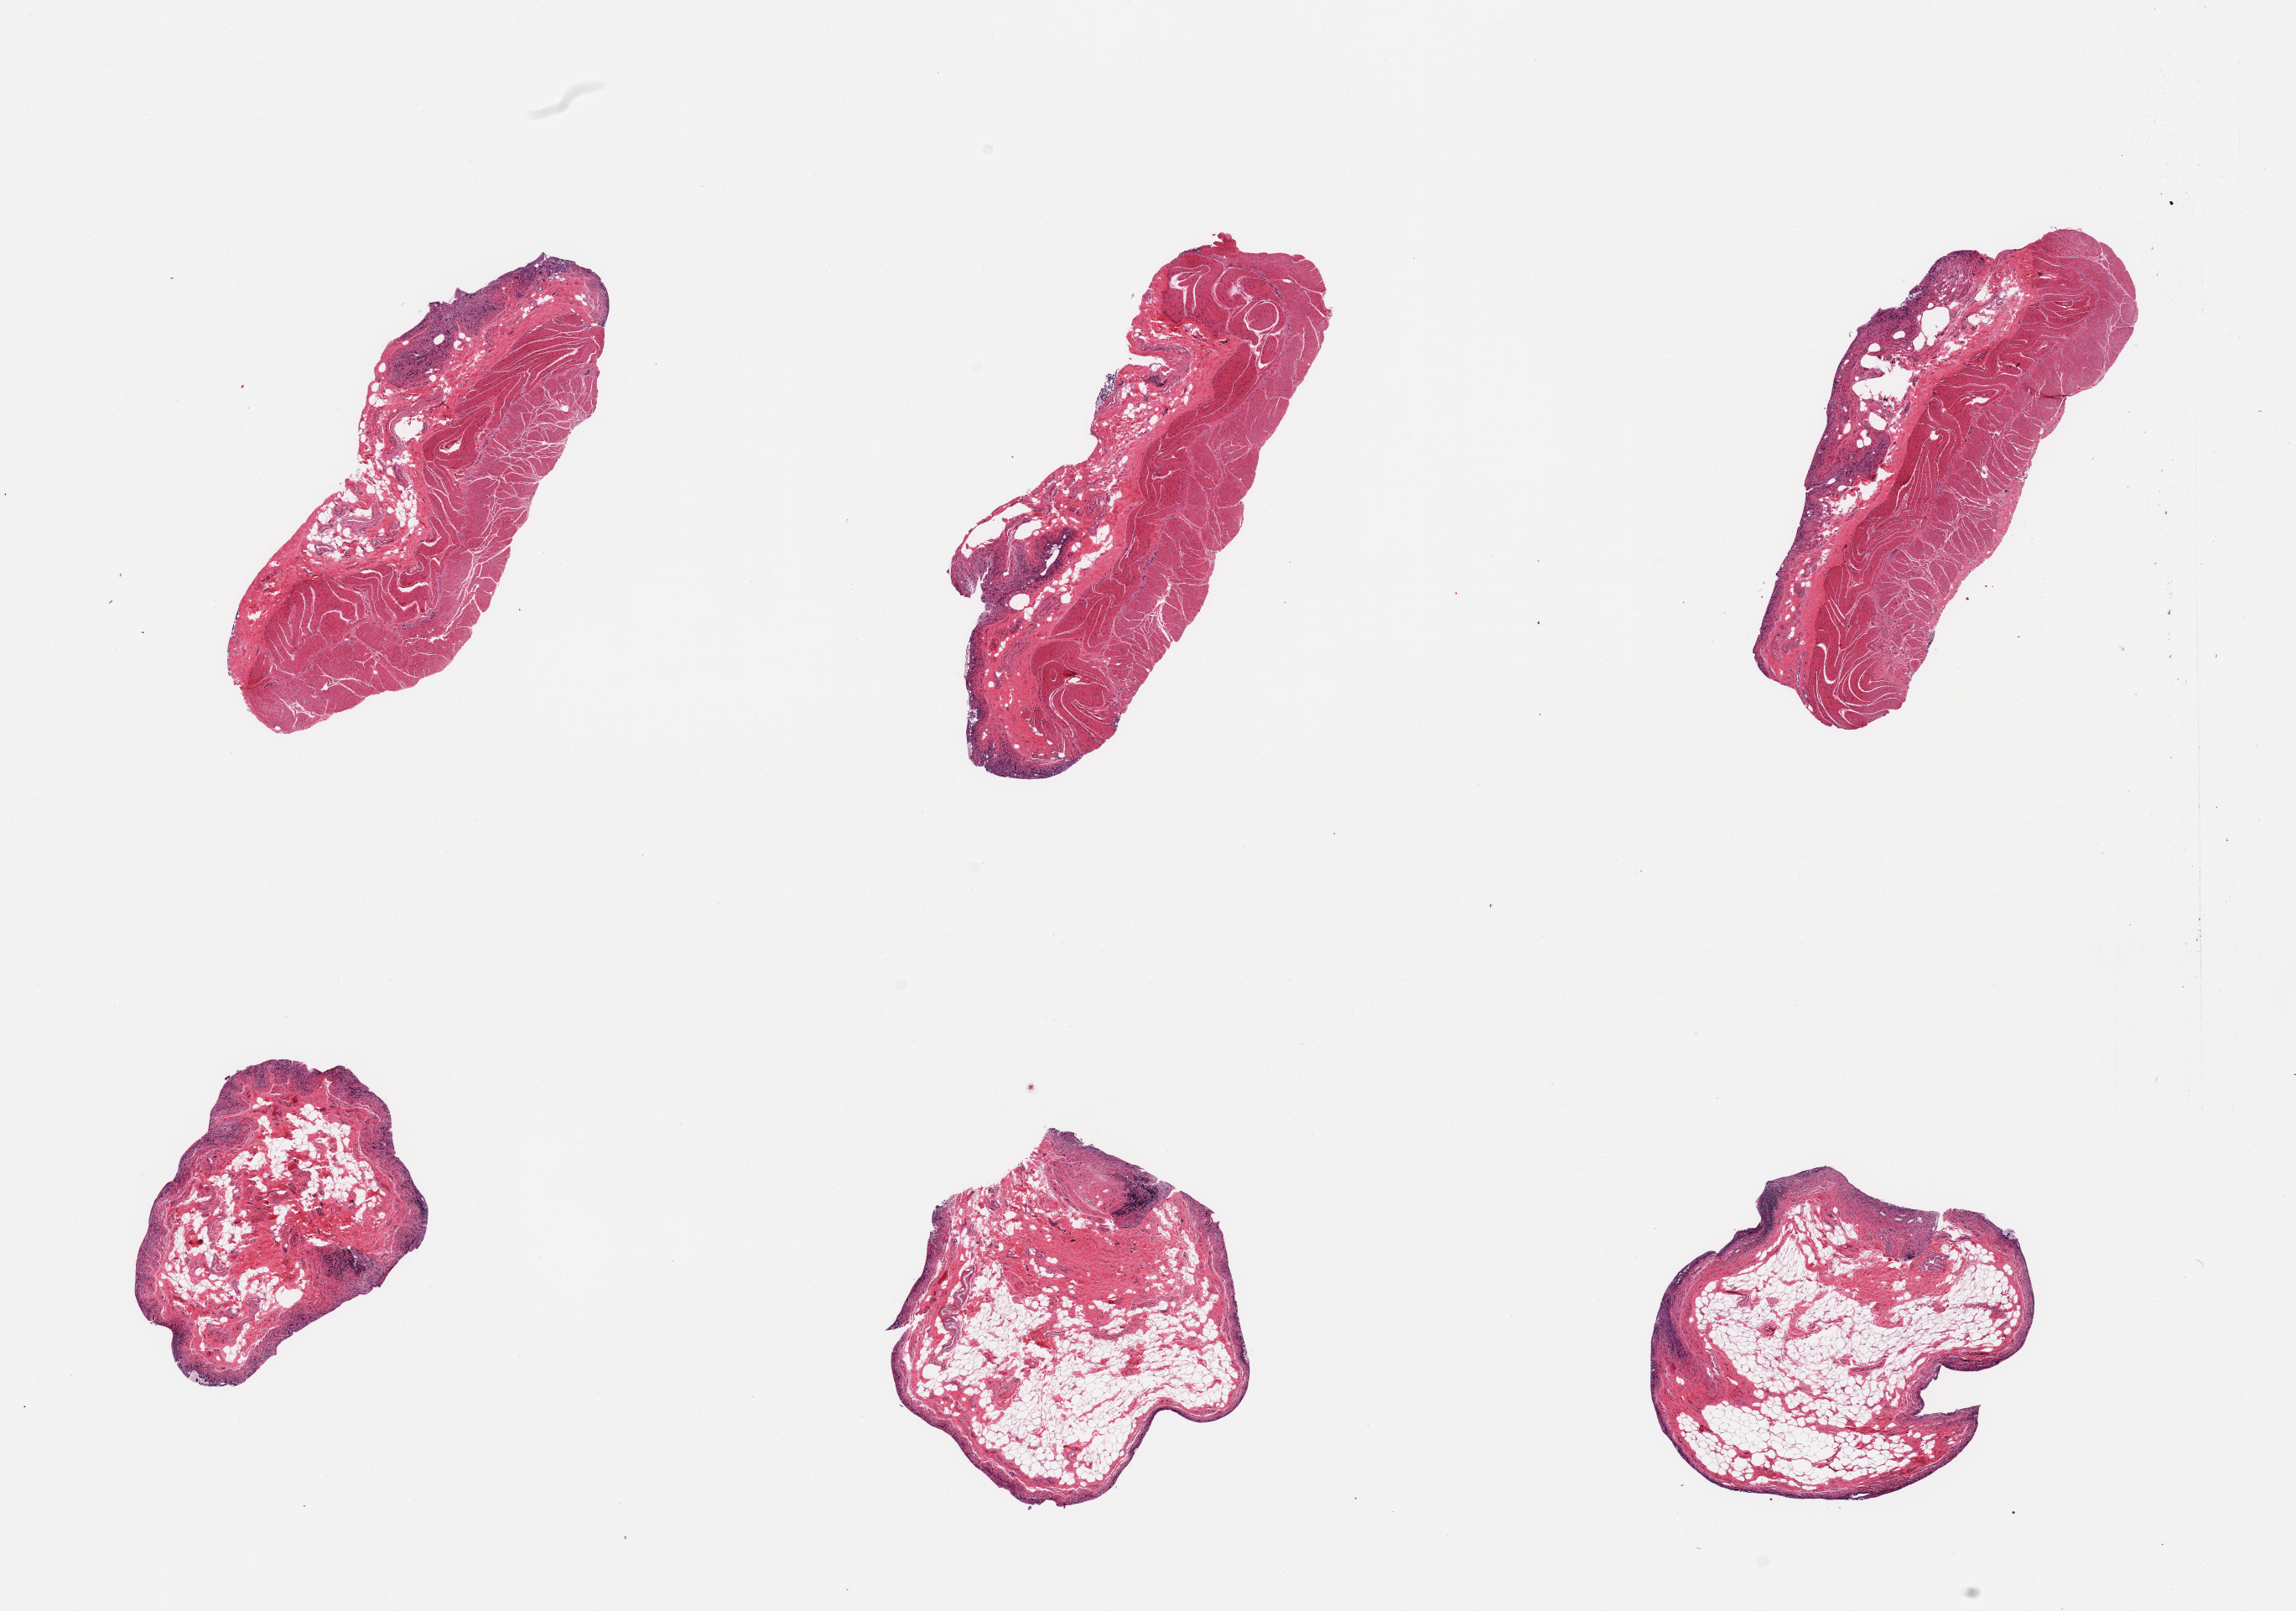
Haematoxylin and eosin whole-slide image, a low-resolution overview of the entire scanned area, about 21.7 x 15.2 mm (slide scanned at 20x); PAXgene-fixed paraffin-embedded (PFPE) section; section of ileum (target tissue); tissue donor sample. Donor: male.
Review note (as recorded): 6 pieces; minimal lymphoid tissue; excessive muscularis.